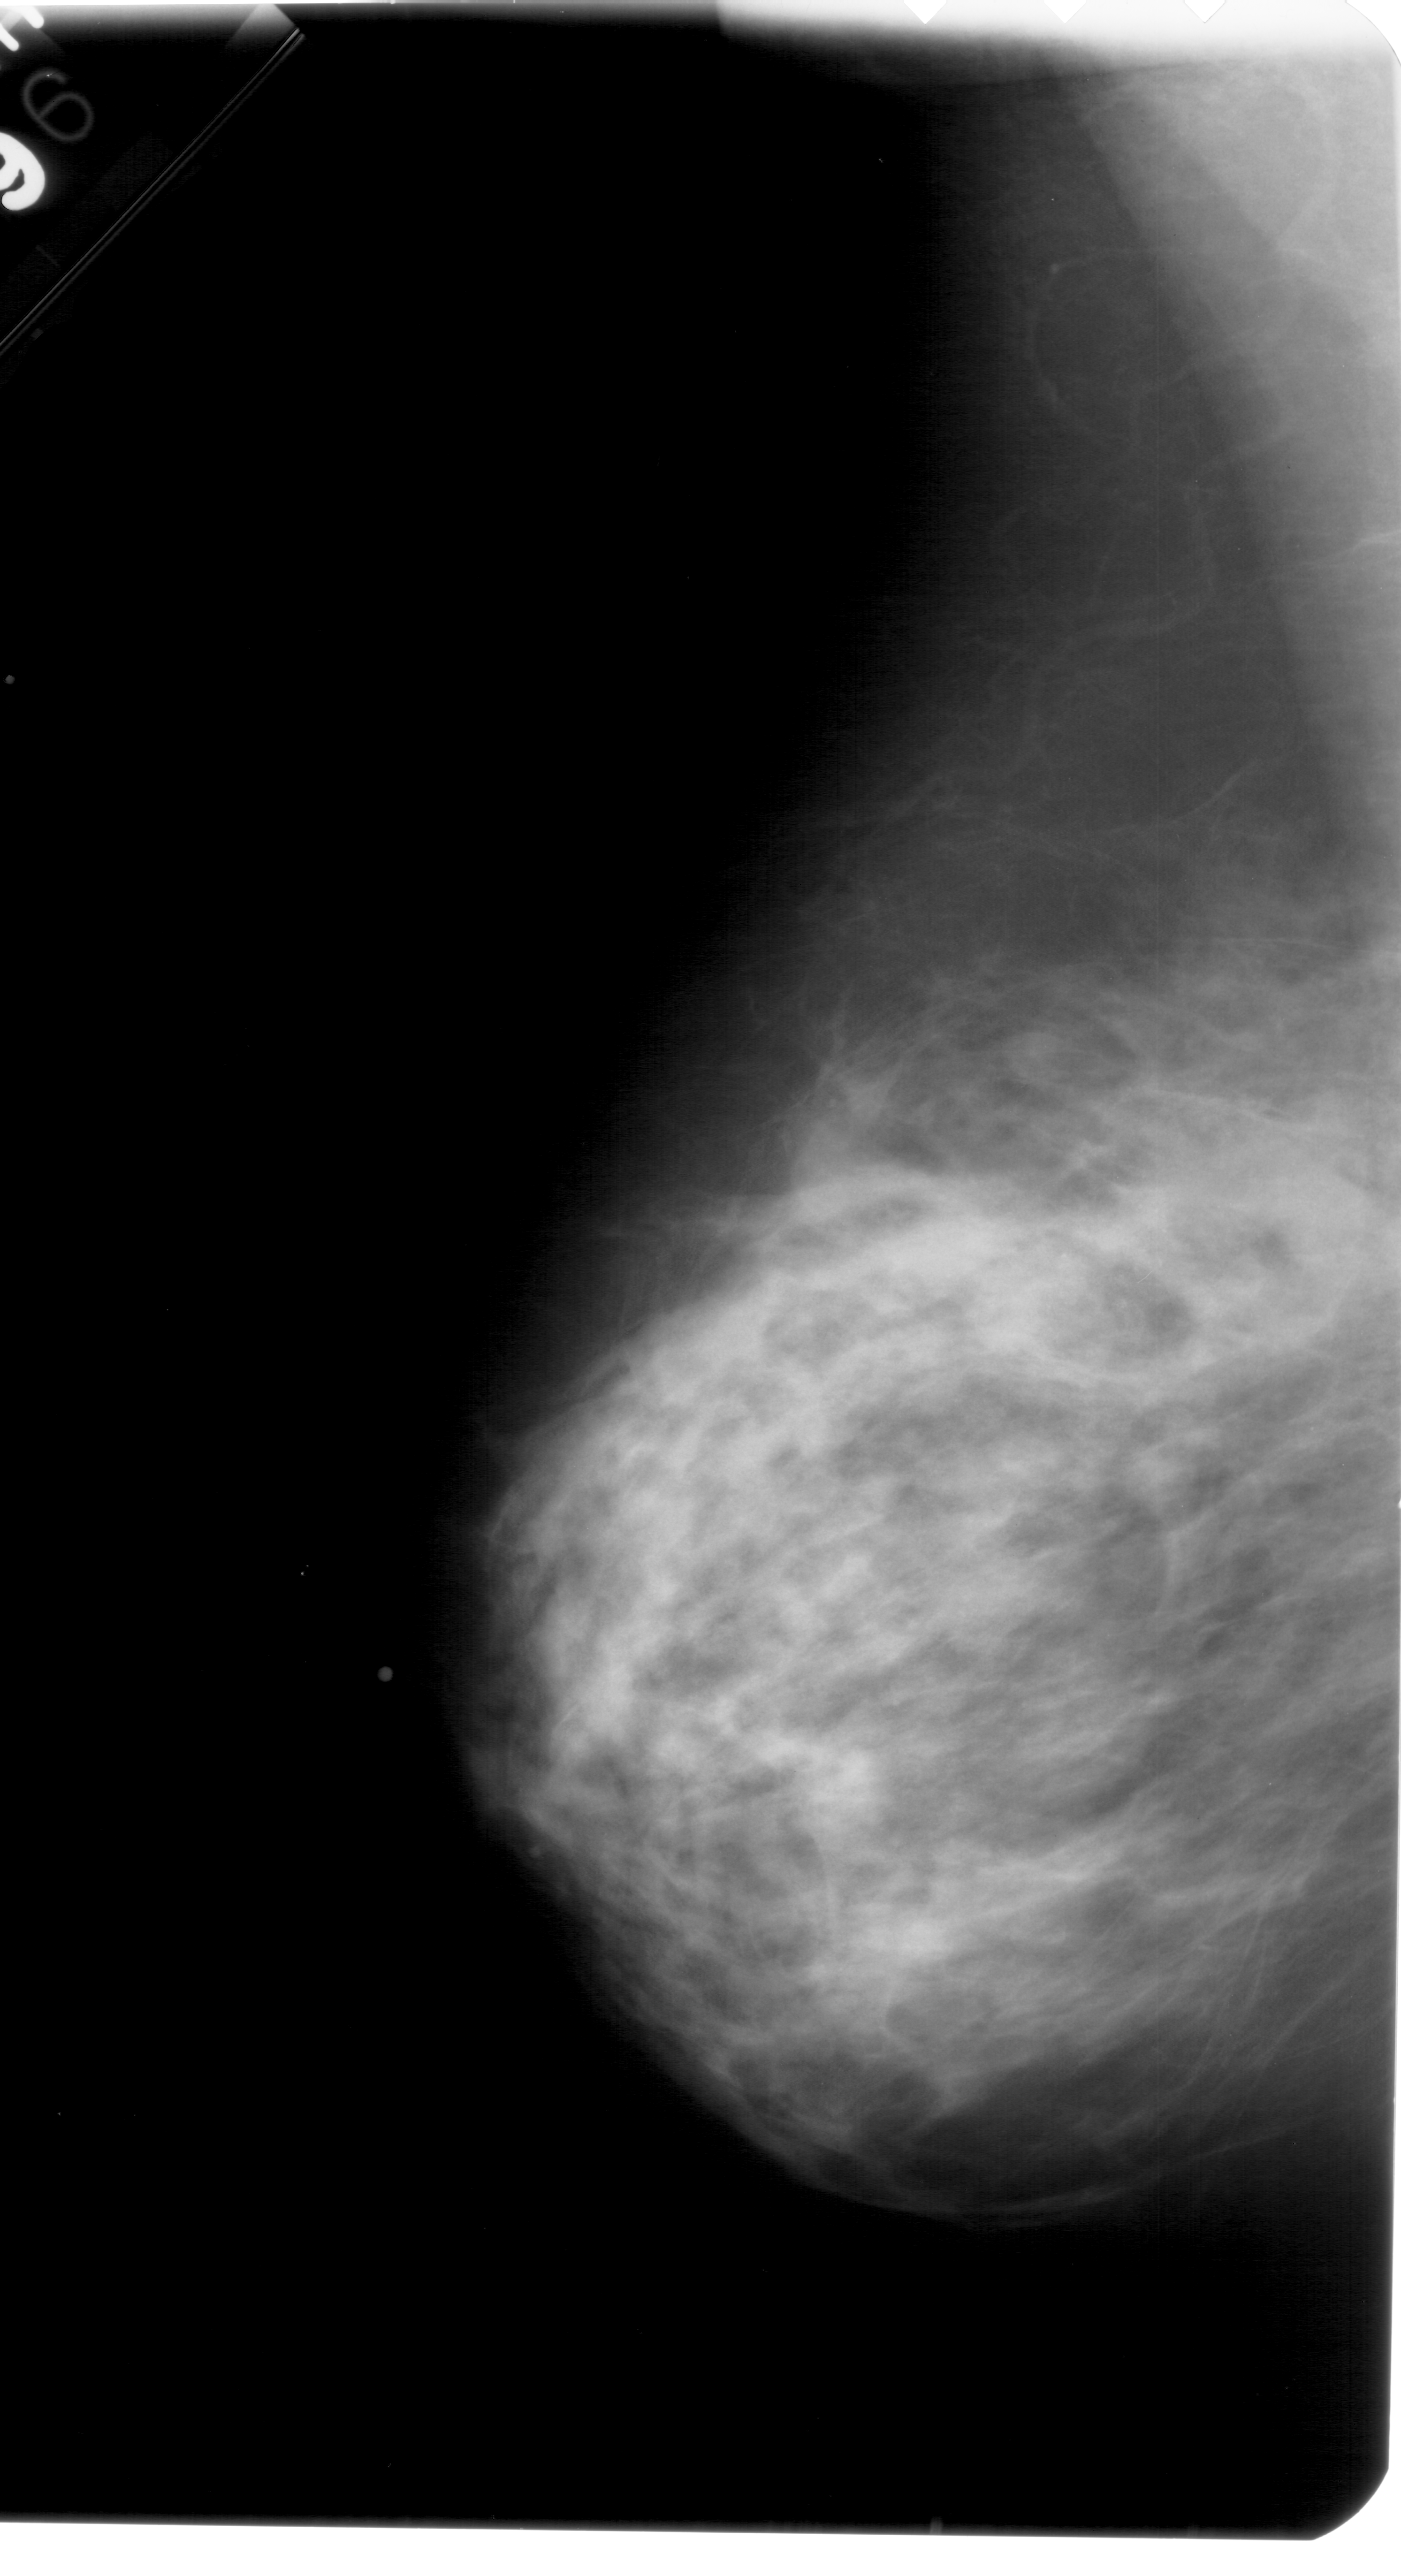
Mammogram (digitized film); left breast; mediolateral oblique (MLO) view; BI-RADS breast density category 4 (scale 1–4).
Marked findings (only marked abnormalities are described; nothing is implied about the rest of the image): calcifications, morphology pleomorphic, distribution clustered; BI-RADS assessment category 4; subtlety rating 1 on a 1 (subtle) to 5 (obvious) scale; pathology (as recorded): malignant.